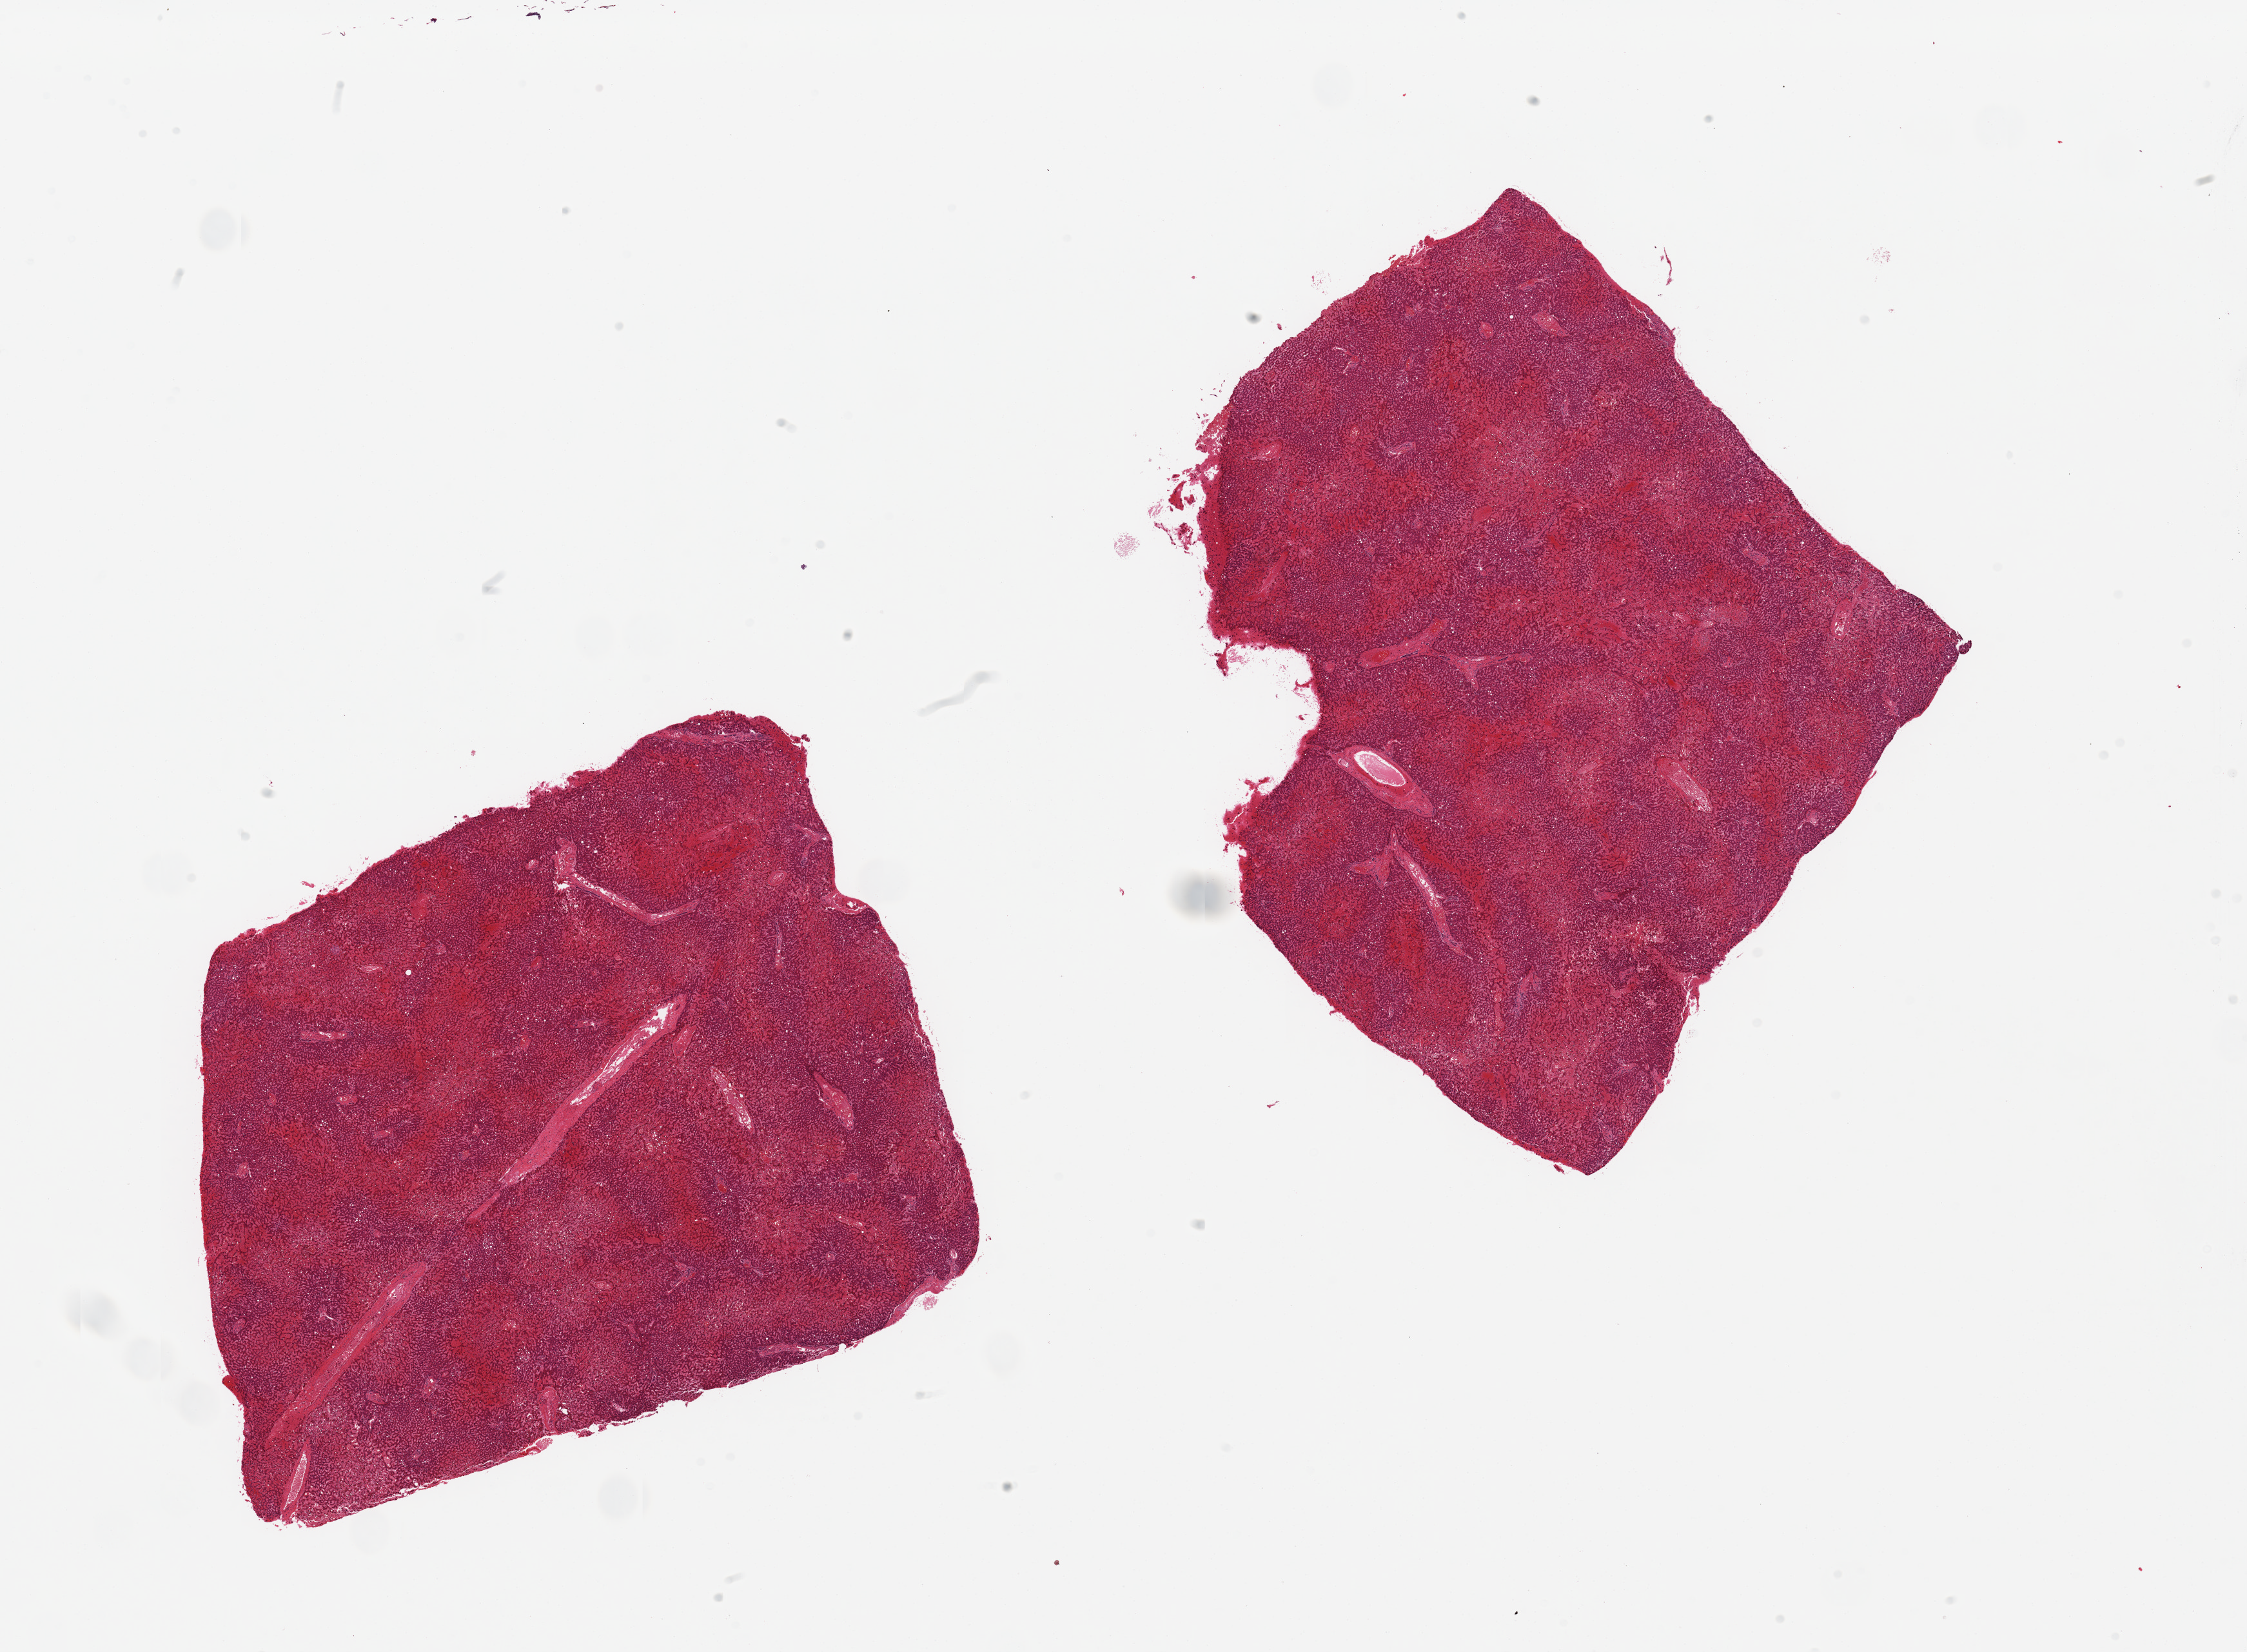
Digitized H&E-stained section, low-resolution overview of the scanned area, about 27.6 x 20.3 mm (from a 20x scan); PAXgene-fixed, paraffin-embedded tissue; section of liver (target tissue); tissue donor sample.
• review note (as recorded): 2 pieces, severe difffuse passive congestion, mild macrovesicular steatosis